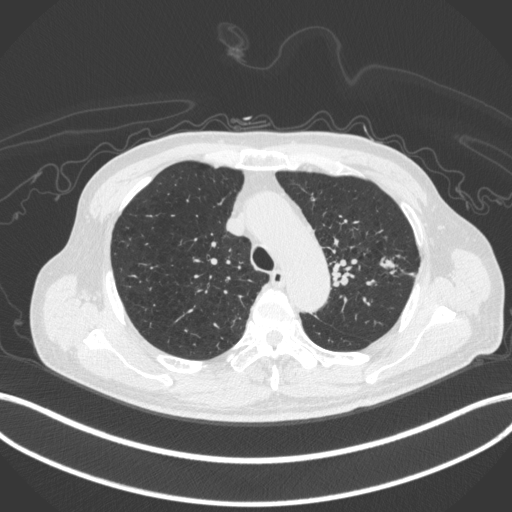
Chest CT, one axial slice; position 329 of 420 along the scan axis; reconstruction kernel B31f; 120 kVp; lung window (W 1500 / L -600 HU); 1 mm slice thickness; 512 × 512 image matrix, field of view 400 × 400 mm. Patient: male, 77 years. Case-level facts recorded for this patient, not image findings: clinical TNM (as recorded): T3 N1 M0.
Annotated regions visible in this slice (bounding box drawn by a radiologist):
- lung tumour (recorded histology: adenocarcinoma): bounding box [x1, y1, x2, y2] px = [378, 254, 397, 273]